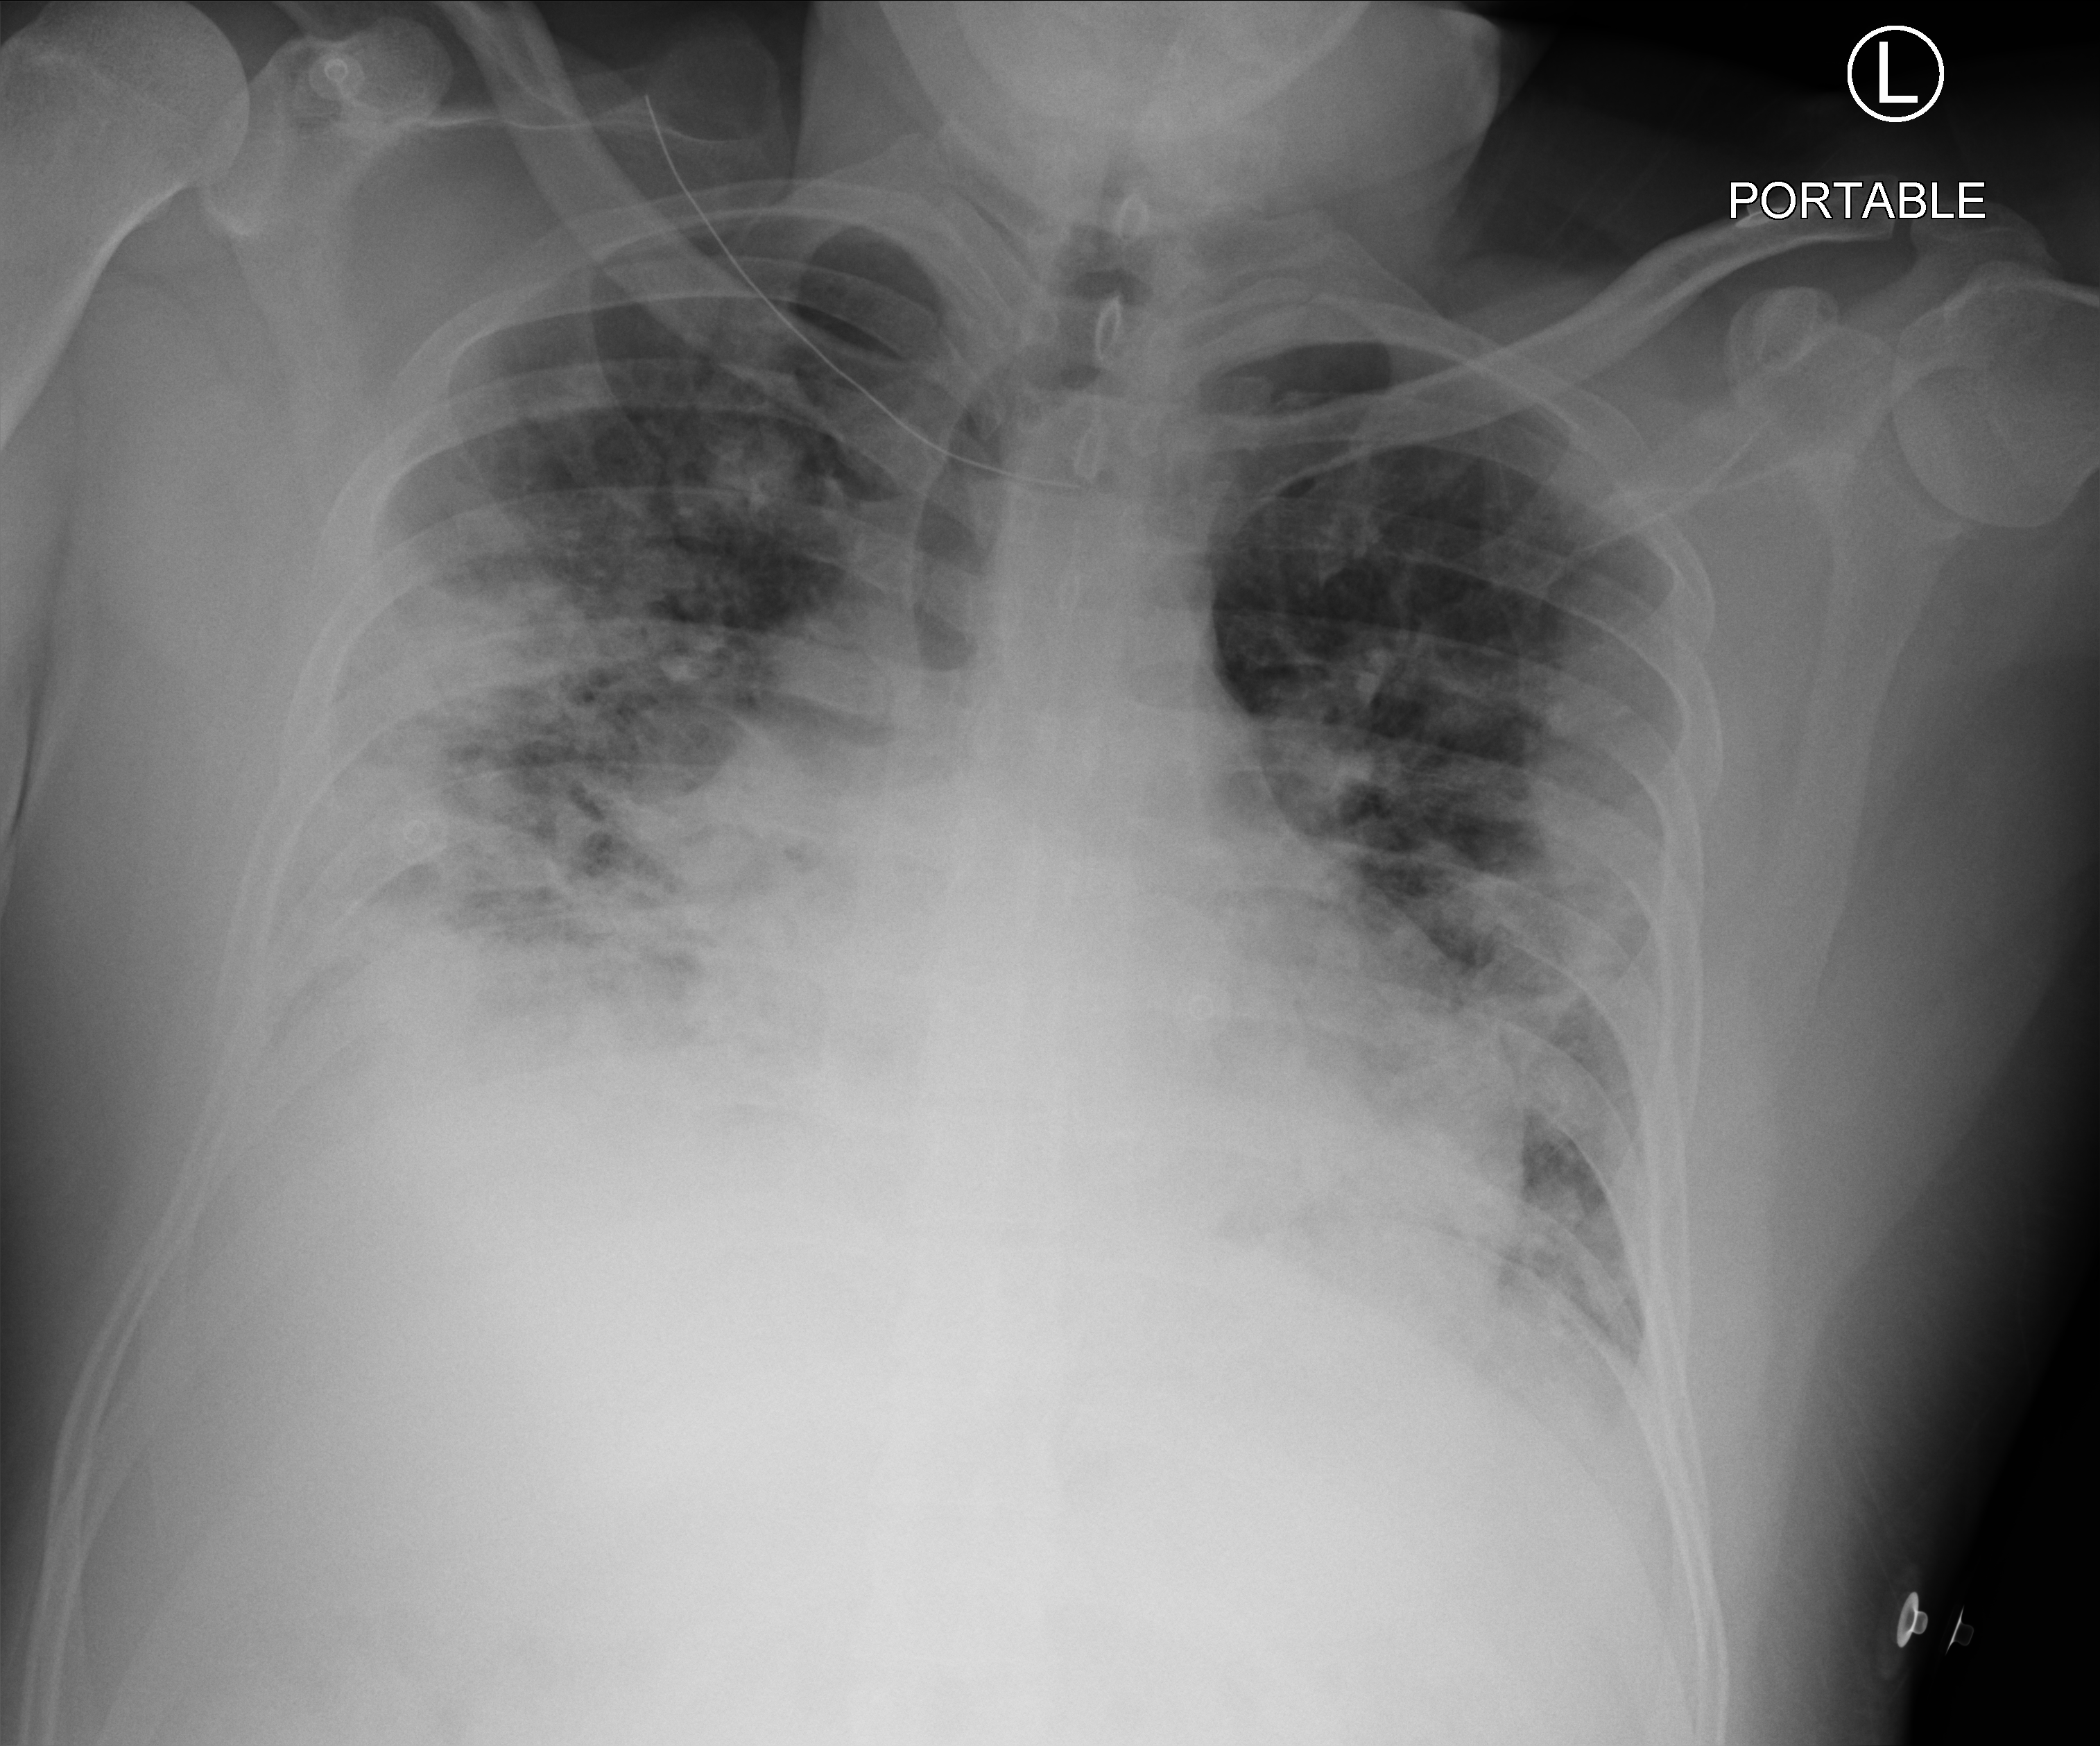
Chest X-ray (portable), anteroposterior (AP) projection. Male patient hospitalised with COVID-19, age 18–59 years.
Hospital-stay facts (about this admission, not read from this image; timing relative to this image not recorded):
- admitted to intensive care during this hospital stay: yes